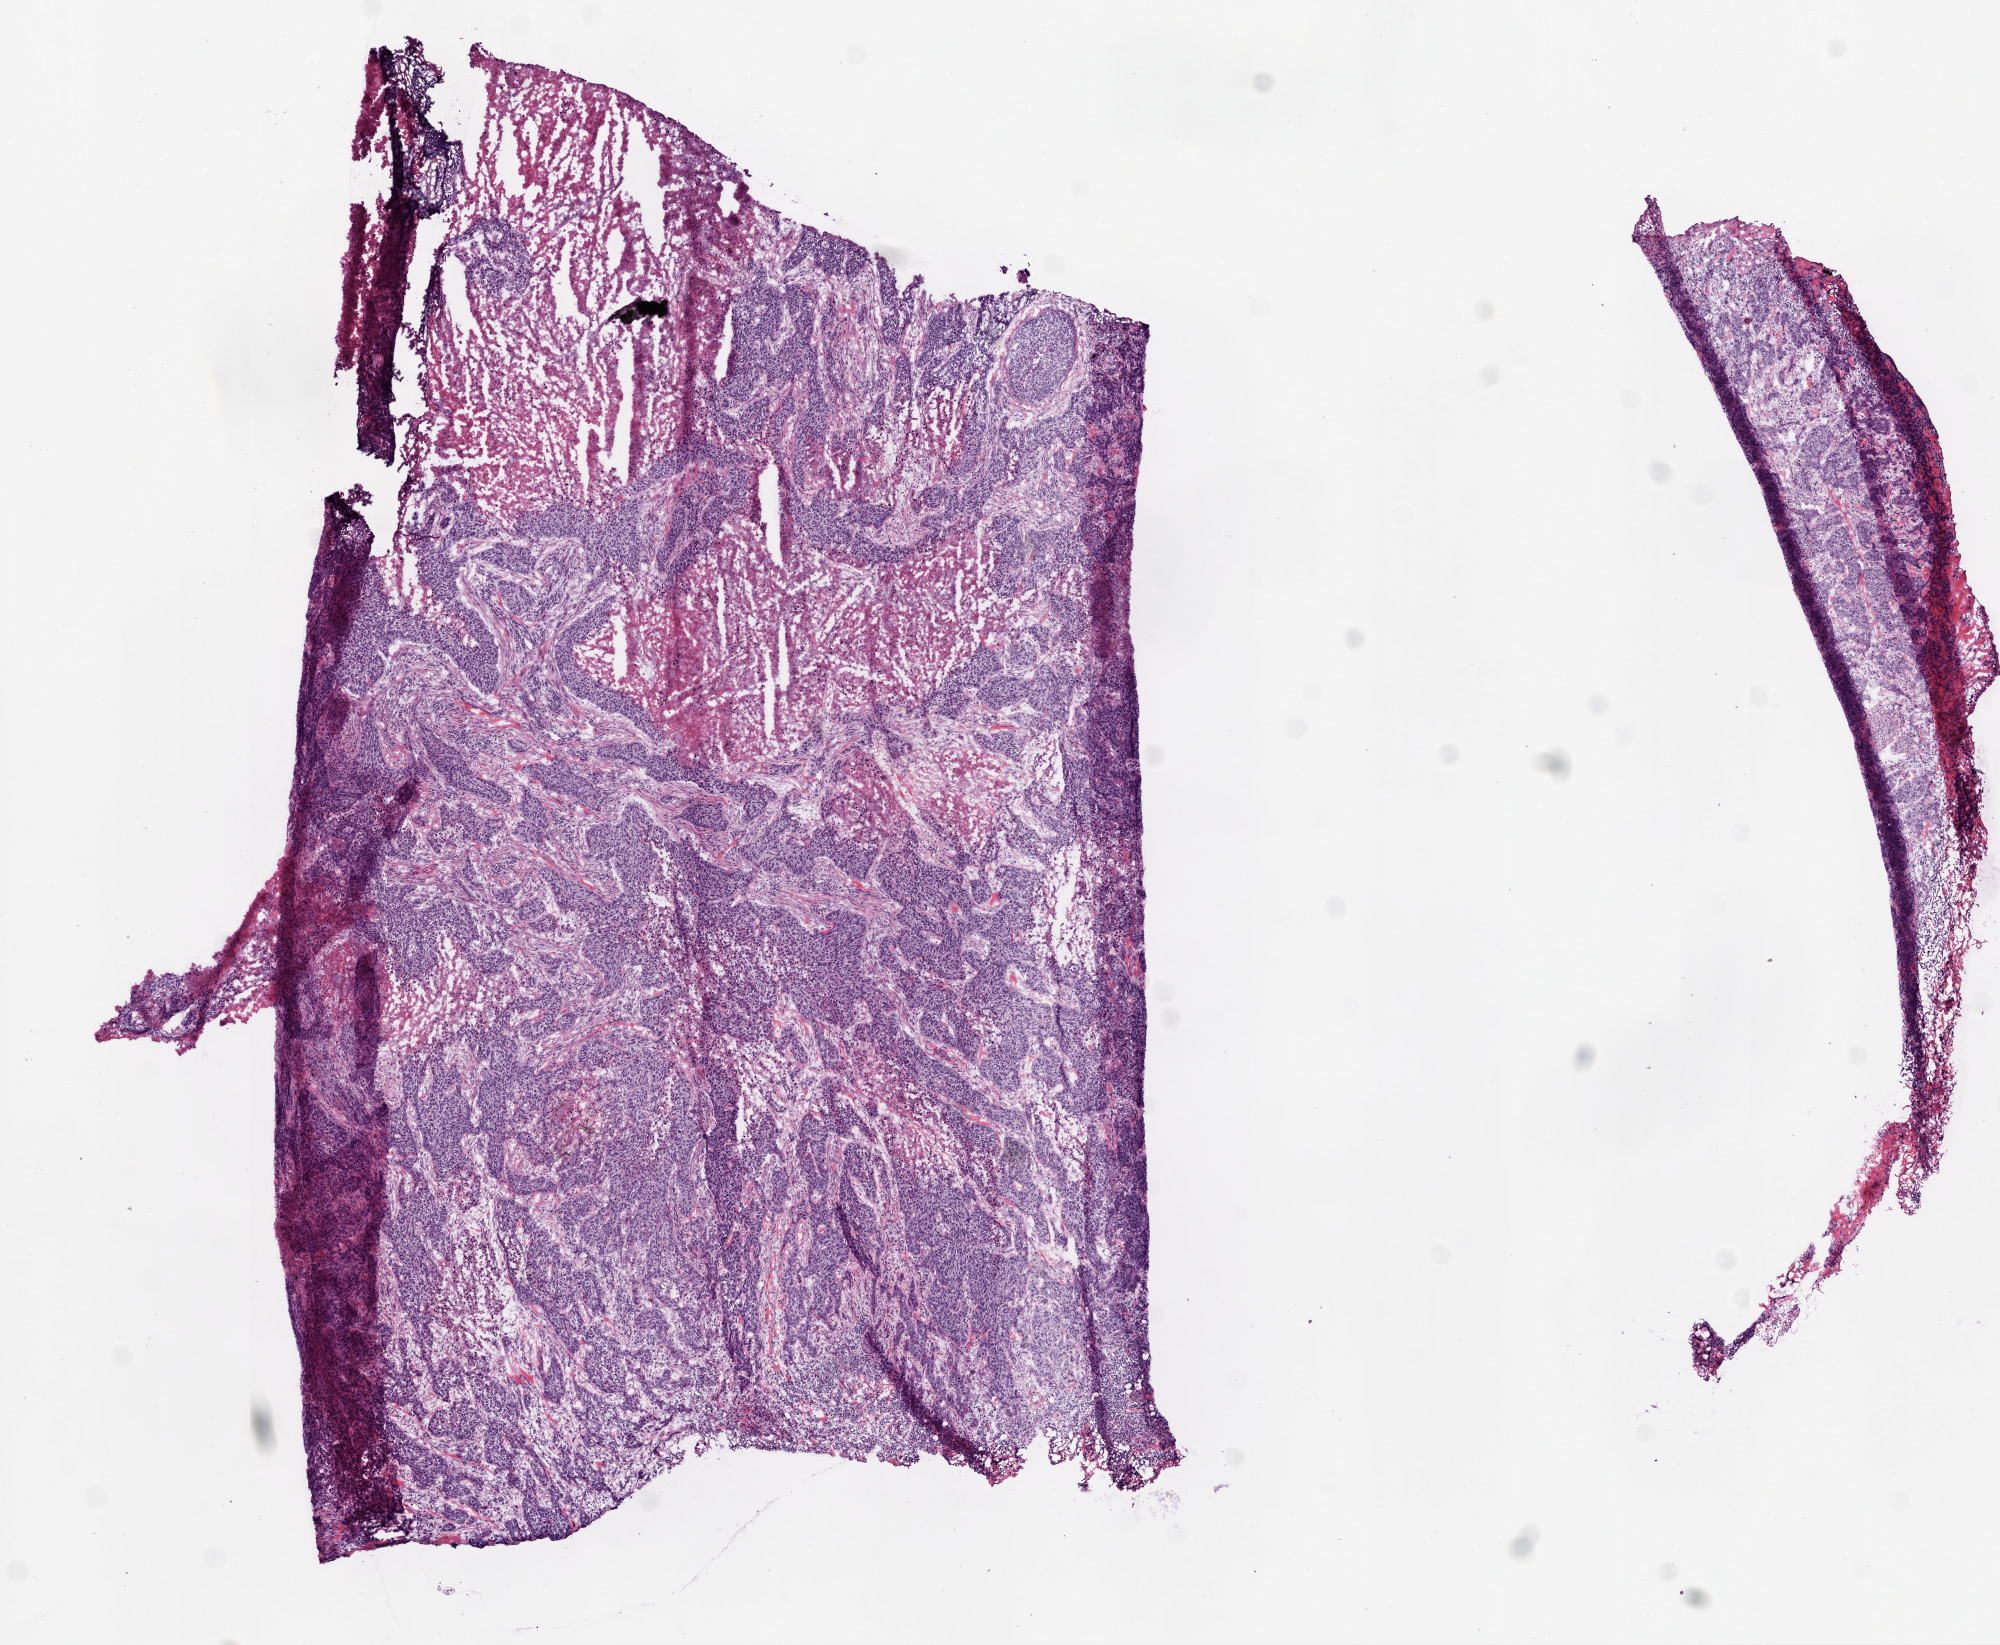
H&E-stained whole-slide image — low-resolution overview of the scanned area, about 8.0 x 6.6 mm. Frozen section from the bottom of the tissue portion. Lung, primary tumour sample. Patient: male, age at initial diagnosis 58 years. Pathologist review of this section (percent, as recorded): tumour cells 70%, tumour nuclei 75%, normal cells 0%, stromal cells 10%, necrosis 20%.
Histologic diagnosis: Squamous cell carcinoma, NOS (lower lobe, lung). AJCC pathologic stage: IIB (6th edition).